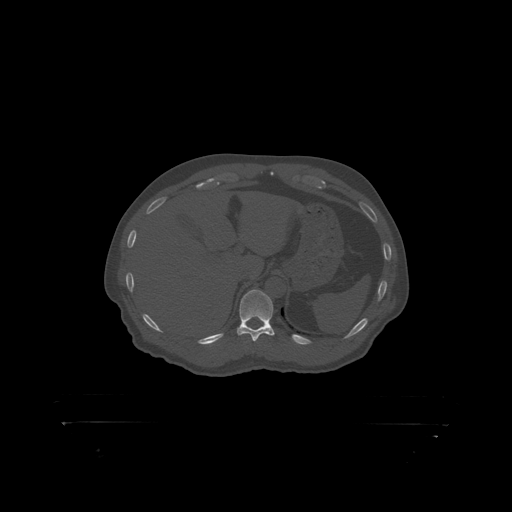
CT including the spine, one axial slice; slice 377 of 399 in the series (ordered by position); reconstruction kernel STANDARD; 120 kVp; bone window (W 1800 / L 400 HU); 1.25 mm slice thickness; 512 × 512 image matrix, field of view 650 × 650 mm. Male patient, age 46 years. From the clinical record (not read from this slice): primary cancer: skin.
Annotated regions visible in this slice (semi-automatically segmented with operator editing):
- T11 vertebra: box from (x=240, y=290) to (x=274, y=319) px